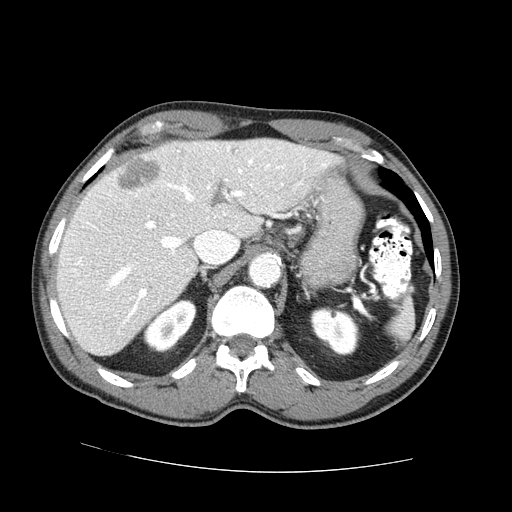
Contrast-enhanced abdominal CT (liver protocol), one axial slice. Slice 50 of 73 in the series (ordered by position). Reconstruction kernel STANDARD. 100 kVp. One of 2 acquisitions stored at this slice position. Soft-tissue window (W 400 / L 40 HU). 2.5 mm slice thickness. 512 × 512 image matrix, field of view 380 × 380 mm. From the clinical record (not read from this slice): diagnosis: hepatocellular carcinoma (patient treated with transarterial chemoembolisation; whether this scan precedes or follows treatment is not stated here); TNM stage (as recorded): Stage-IVA; Child-Pugh class: A; tumour nodularity: uninodular.
Outlined on this slice (semi-automatically segmented with operator editing):
- liver parenchyma outside the tumour (the mass and vessels are separate outlines, so this box may not span the whole liver): bounding box (x1, y1, x2, y2) in pixels: (56, 138, 341, 356)
- mass: (119, 155, 160, 189)
- liver vessels: (69, 146, 327, 323)